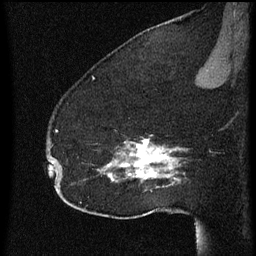
Breast MRI (dynamic contrast-enhanced), one sagittal slice. Dynamic contrast-enhanced series, image 2 of 3 at this slice position (ordered by acquisition). 1.5 T. TE 4.2 ms, TR 8 ms. 2 mm slice thickness. 256 × 256 image matrix, field of view 180 × 180 mm. Patient: female, 52 years.
Outlined on this slice (semi-automatically segmented with operator editing):
- analysis volume of interest (the breast-tissue region the enhancement analysis was run in; not a lesion): bounding box <54,130,178,207> (left, top, right, bottom; pixels)
- tumour enhancement mask (voxels above the 70 % enhancement threshold inside the analysis volume of interest): <54,130,178,189>